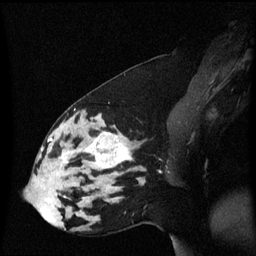
Breast MRI (dynamic contrast-enhanced), one sagittal slice; position 25 of 60 along the scan axis; dynamic contrast-enhanced series, image 2 of 3 at this slice position (ordered by acquisition); 1.5 T; TE 4.2 ms, TR 8.4 ms; 2 mm slice thickness; 256 × 256 image matrix, field of view 210 × 210 mm. Female patient, age 33 years. Case-level facts recorded for this patient, not image findings: setting: breast cancer imaged before/during neoadjuvant chemotherapy; receptor status: triple-negative.
Annotated regions visible in this slice (semi-automatic segmentation, software-assisted and operator-edited):
- analysis volume of interest (the breast-tissue region the enhancement analysis was run in; not a lesion): box from (x=44, y=123) to (x=139, y=189) px
- tumour enhancement mask (voxels above the 70 % enhancement threshold inside the analysis volume of interest): (x=61, y=132)–(x=132, y=170)